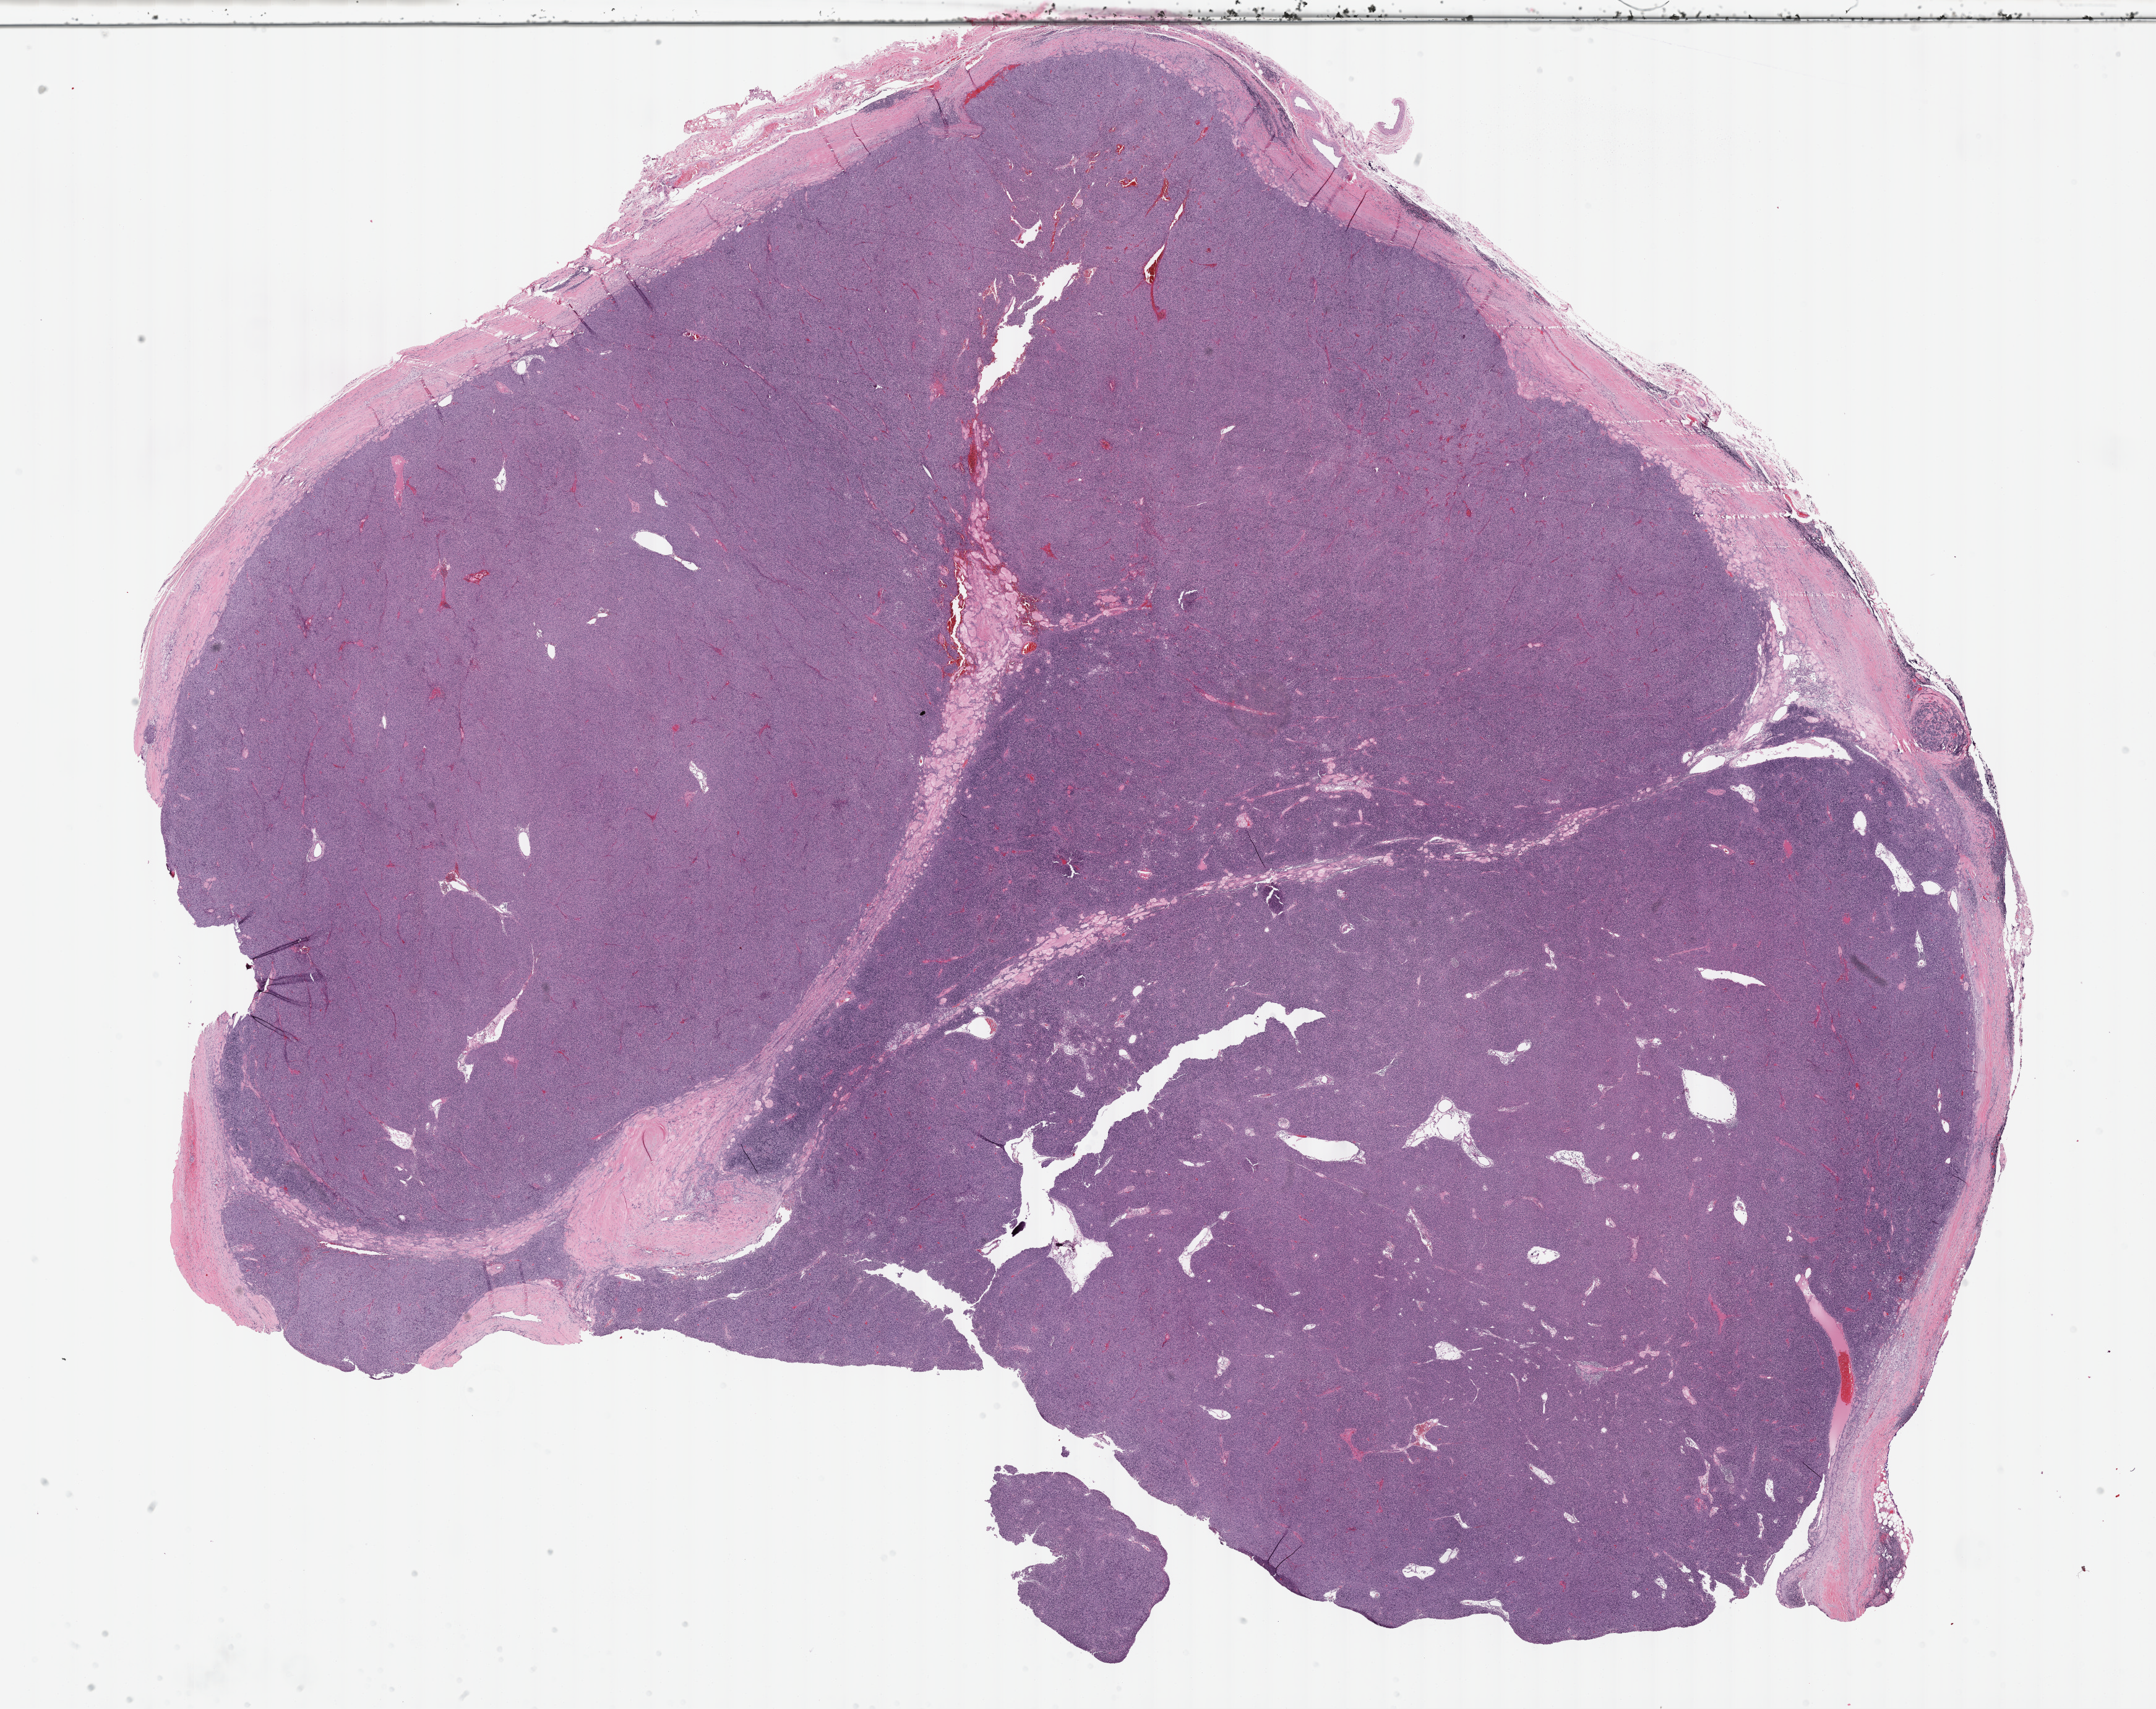
Whole-slide histology image, Hematoxylin and eosin (H&E) stained — low-resolution overview of the scanned area, about 28.2 x 22.3 mm (slide scanned at 40x); FFPE section; thymus, primary tumour sample. Patient: male, age at initial diagnosis 77 years.
Pathologic diagnosis: Thymoma, type B2, malignant.